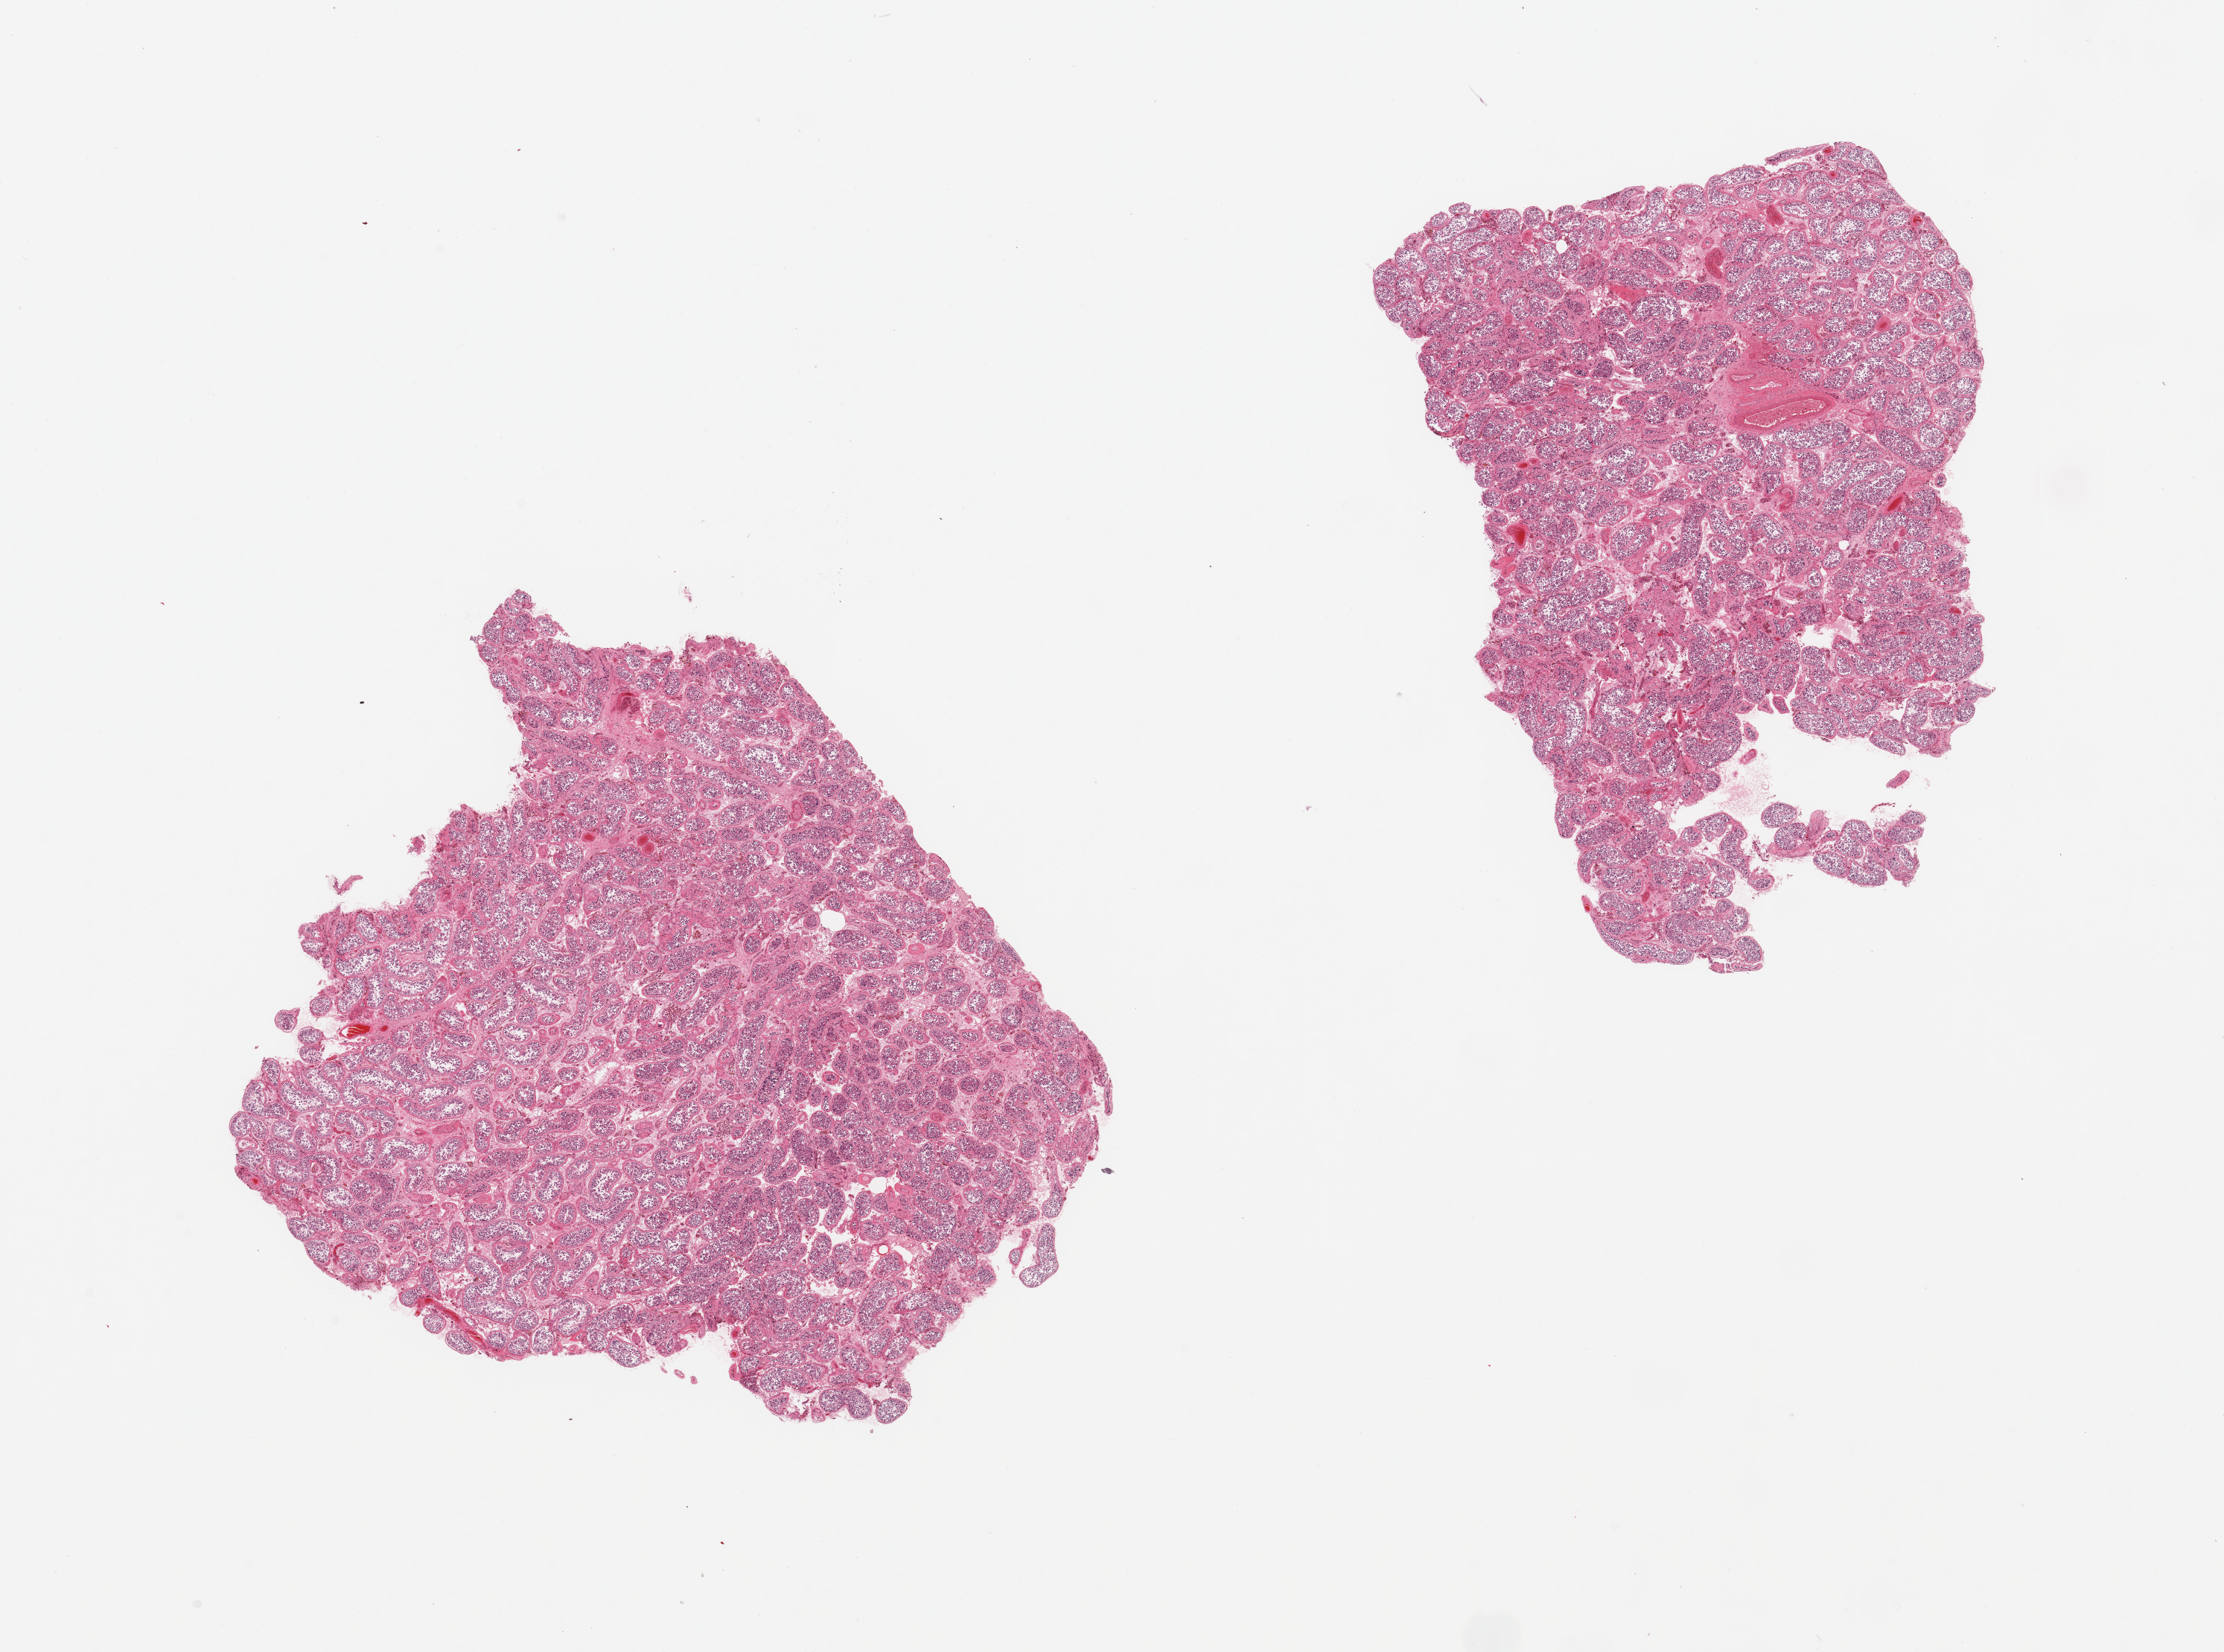
Hematoxylin and eosin (H&E) whole-slide image, low-resolution overview of the scanned area, about 23.6 x 17.6 mm (slide scanned at 20x), PAXgene-fixed paraffin-embedded (PFPE) section, section of testis (target tissue), tissue donor sample. Donor: male.
• reviewer comment on this tissue sample: 2 pieces; spermatogenesis is reduced/absent